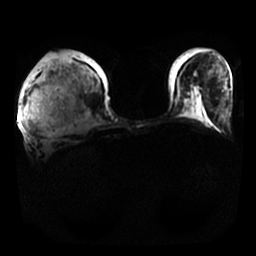
Breast MRI, one axial slice. Slice 3 of 25 in the series (ordered by position). Diffusion-weighted series; image 2 of 4 stored at this slice position (different b-values; order by instance number). 1.5 T. 4 mm slice thickness. 256 × 256 image matrix, field of view 350 × 350 mm. Female patient.
Outlined on this slice (outlined manually by an expert reader):
- tumour on diffusion-weighted imaging: bounding box (x1, y1, x2, y2) in pixels: (31, 84, 55, 115)